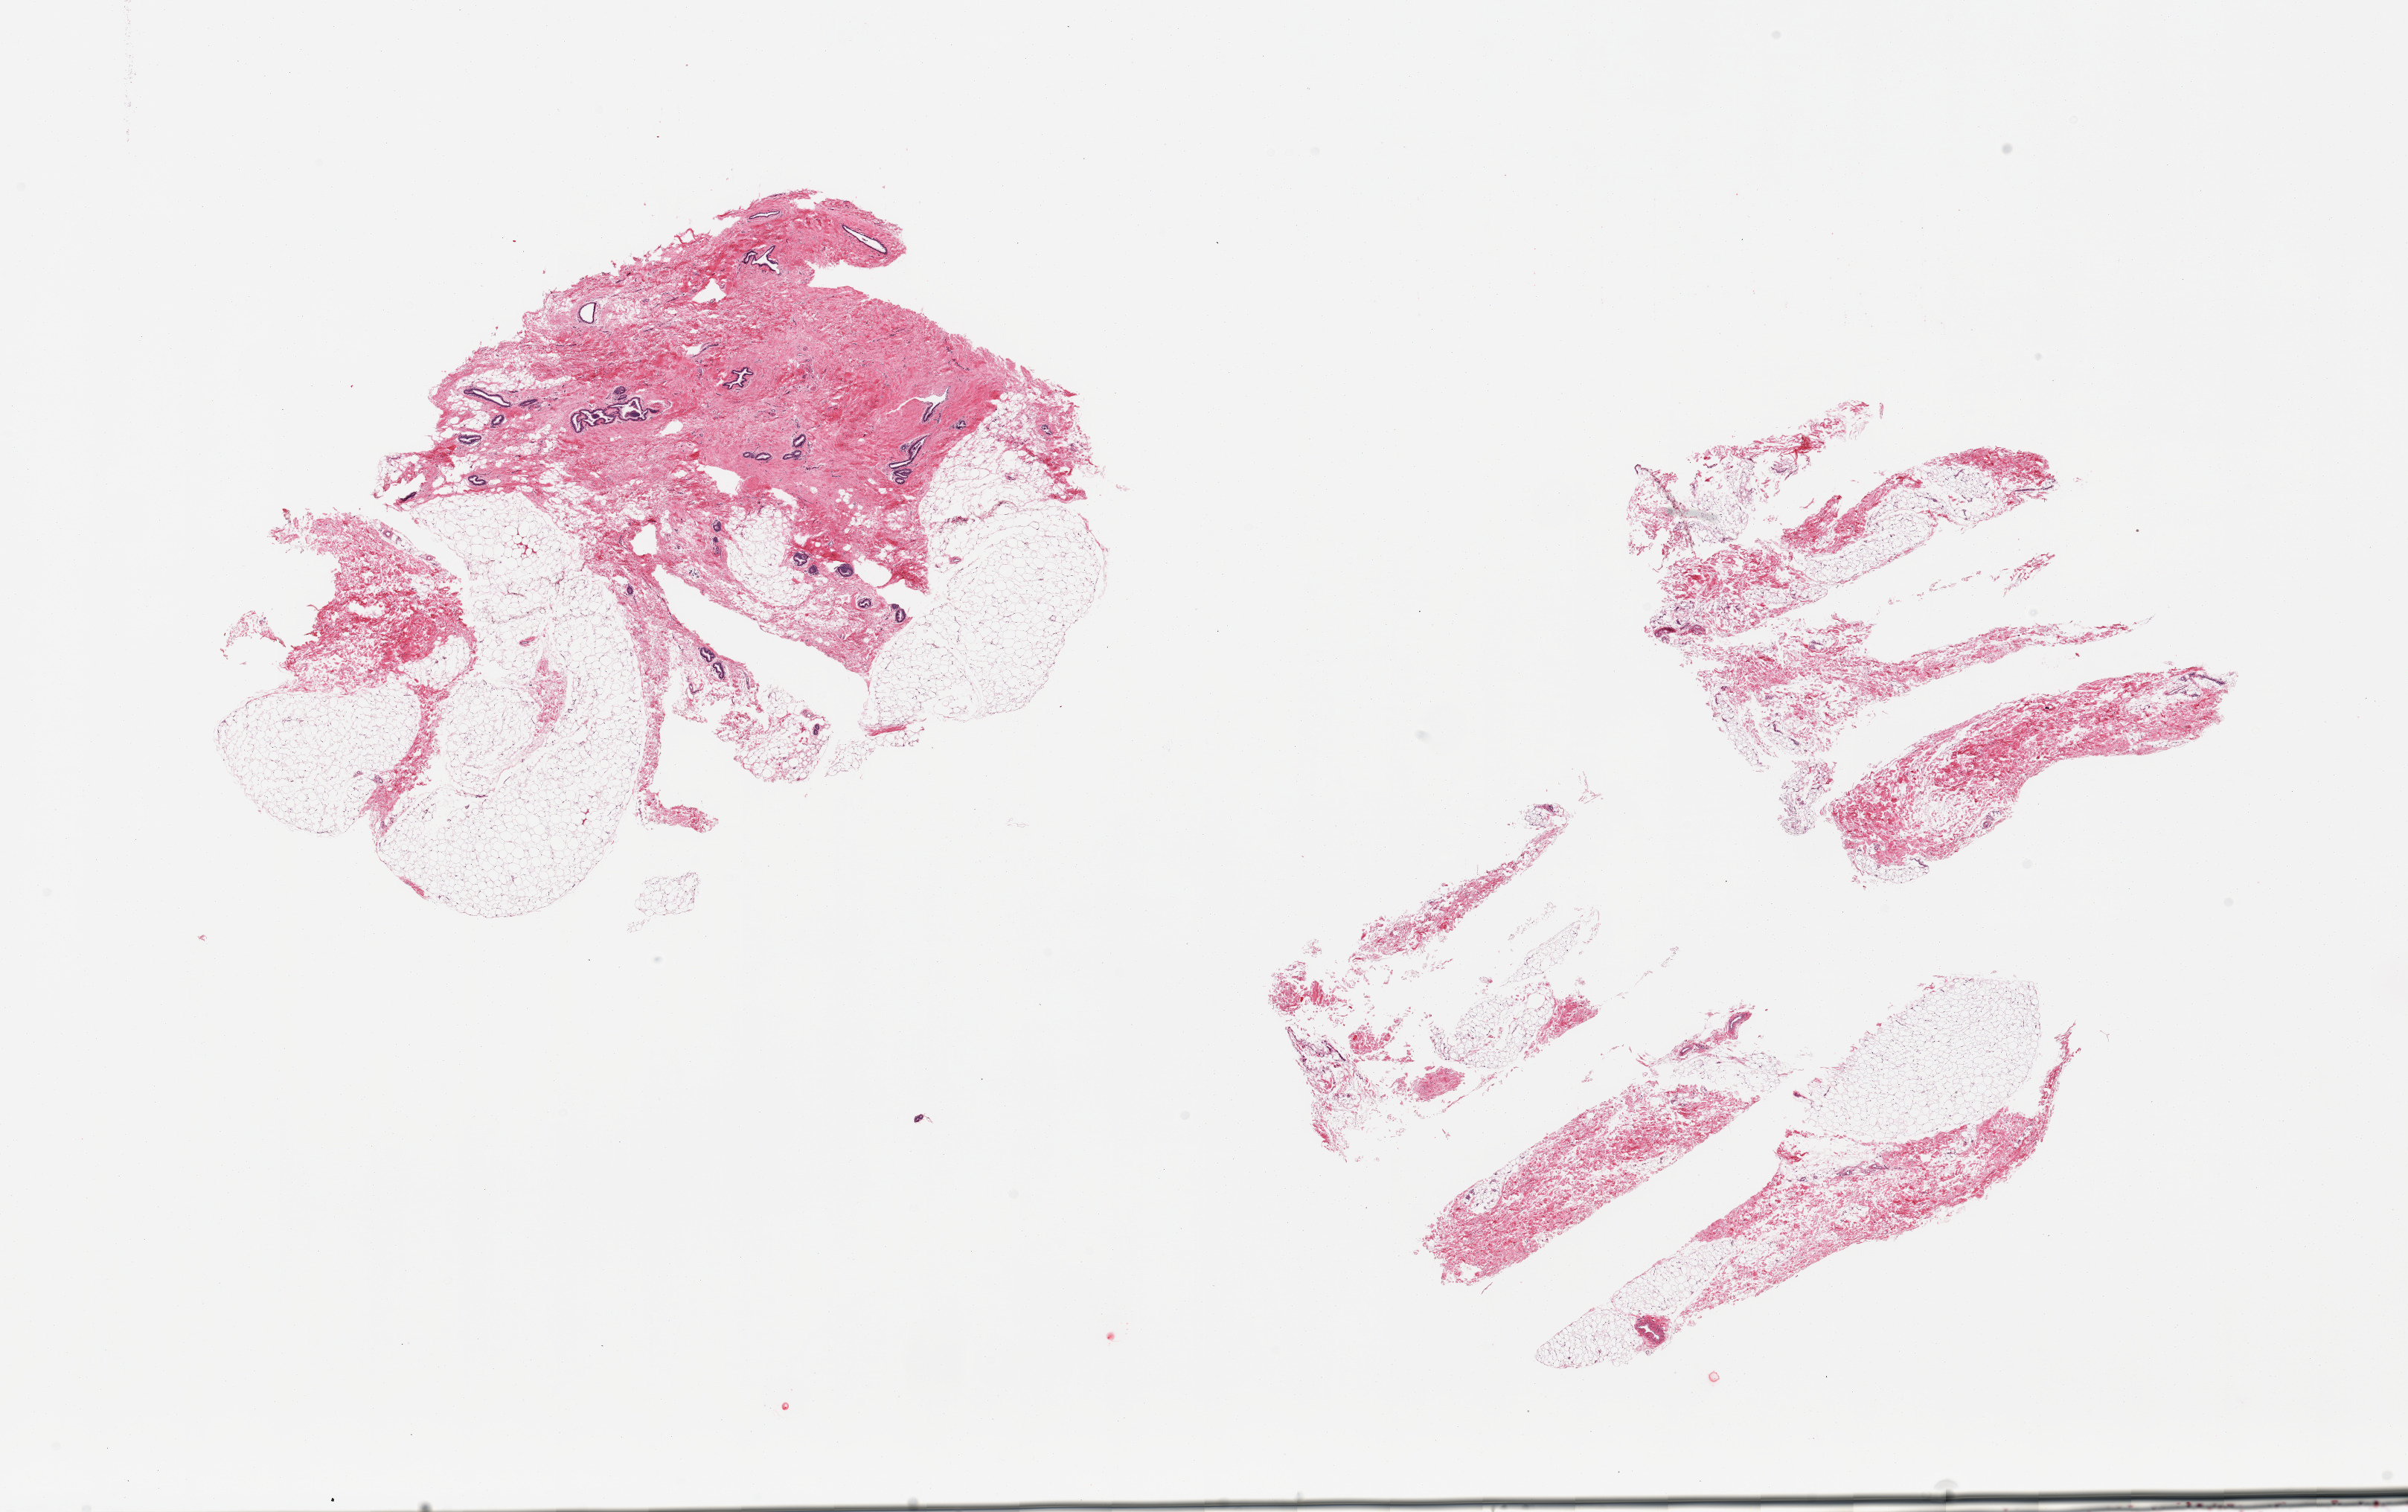
Digitized haematoxylin and eosin-stained section — shown as a low-resolution overview of the whole scanned area (about 25.6 x 16.1 mm, acquisition: 20x scan); PAXgene-fixed paraffin-embedded (PFPE) section; section of breast (target tissue); donor tissue sample.
Reviewer comment on this tissue sample: 2 pieces (fragmented); 1 piece is fragmented fibroadipose tissue, 2nd piece is 50% fat/50% fibrocollagenous tissue with ducts.